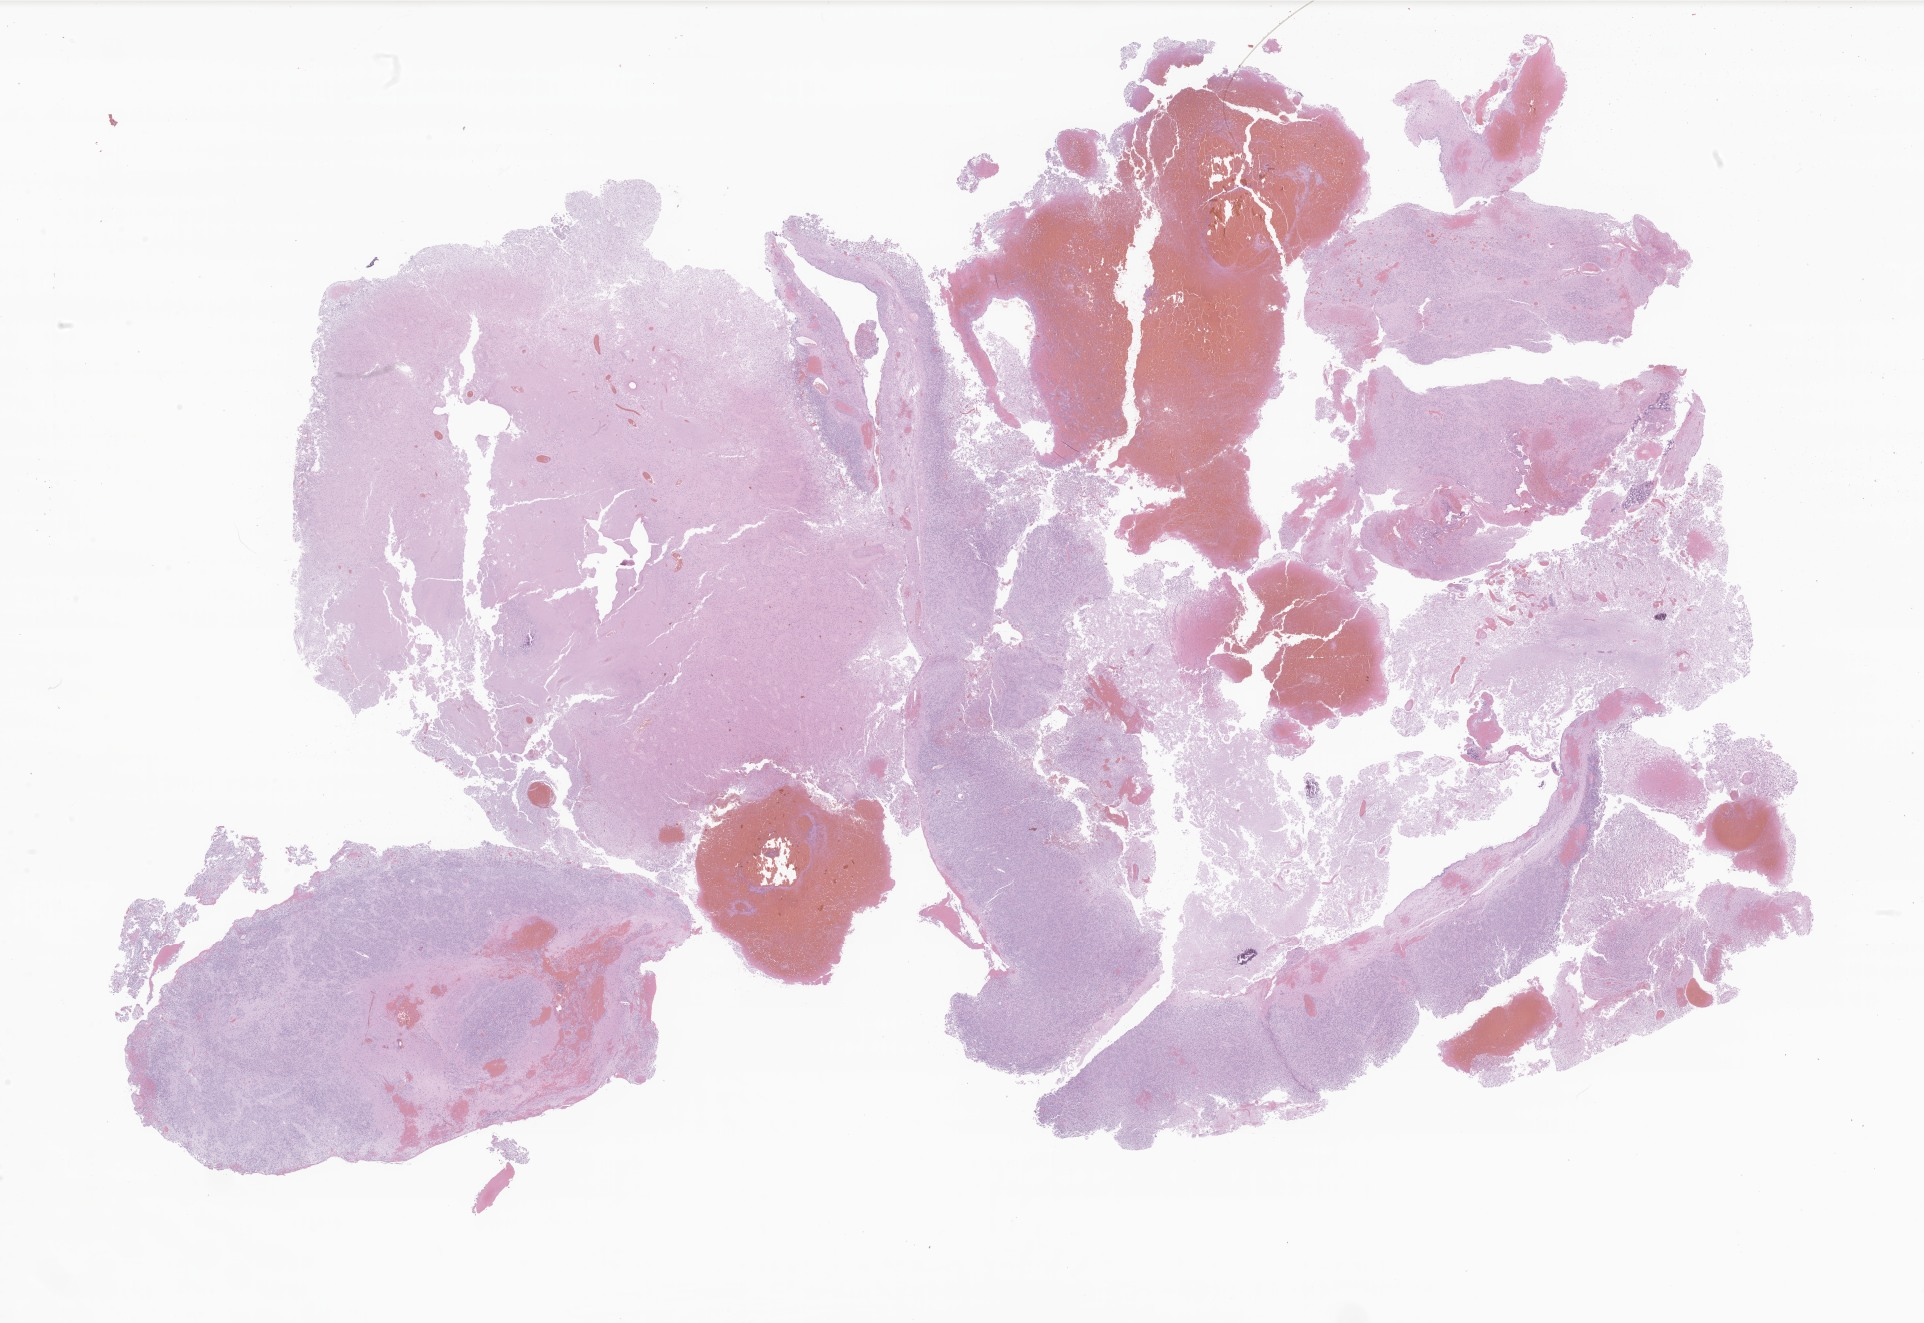
Hematoxylin and eosin (H&E) whole-slide image of tumor tissue from the brain, a low-resolution overview of the entire scanned area, about 32.4 x 22.3 mm, FFPE section. Patient male; age 55 months (4 years 7 months).
Recorded diagnosis: Neoplasm, uncertain whether benign or malignant.